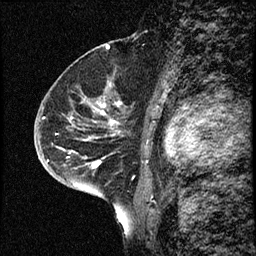
Breast MRI (dynamic contrast-enhanced), one sagittal slice; position 45 of 68 along the scan axis; dynamic contrast-enhanced study with each time point stored as its own series, time point 2 of 3 at this slice position (early post-contrast, ordered by acquisition time); 1.5 T; TE 4.2 ms, TR 17.6 ms; 2 mm slice thickness; 256 × 256 image matrix, field of view 200 × 200 mm. Patient: female, 52 years. Case-level facts recorded for this patient, not image findings: setting: breast cancer imaged before/during neoadjuvant chemotherapy; receptor status: HER2-positive.
Annotated regions visible in this slice (semi-automatically segmented with operator editing):
- analysis volume of interest (the breast-tissue region the enhancement analysis was run in; not a lesion): box from (x=50, y=61) to (x=130, y=184) px
- tumour enhancement mask (voxels above the 100 % enhancement threshold inside the analysis volume of interest): (x=93, y=110)–(x=104, y=167)